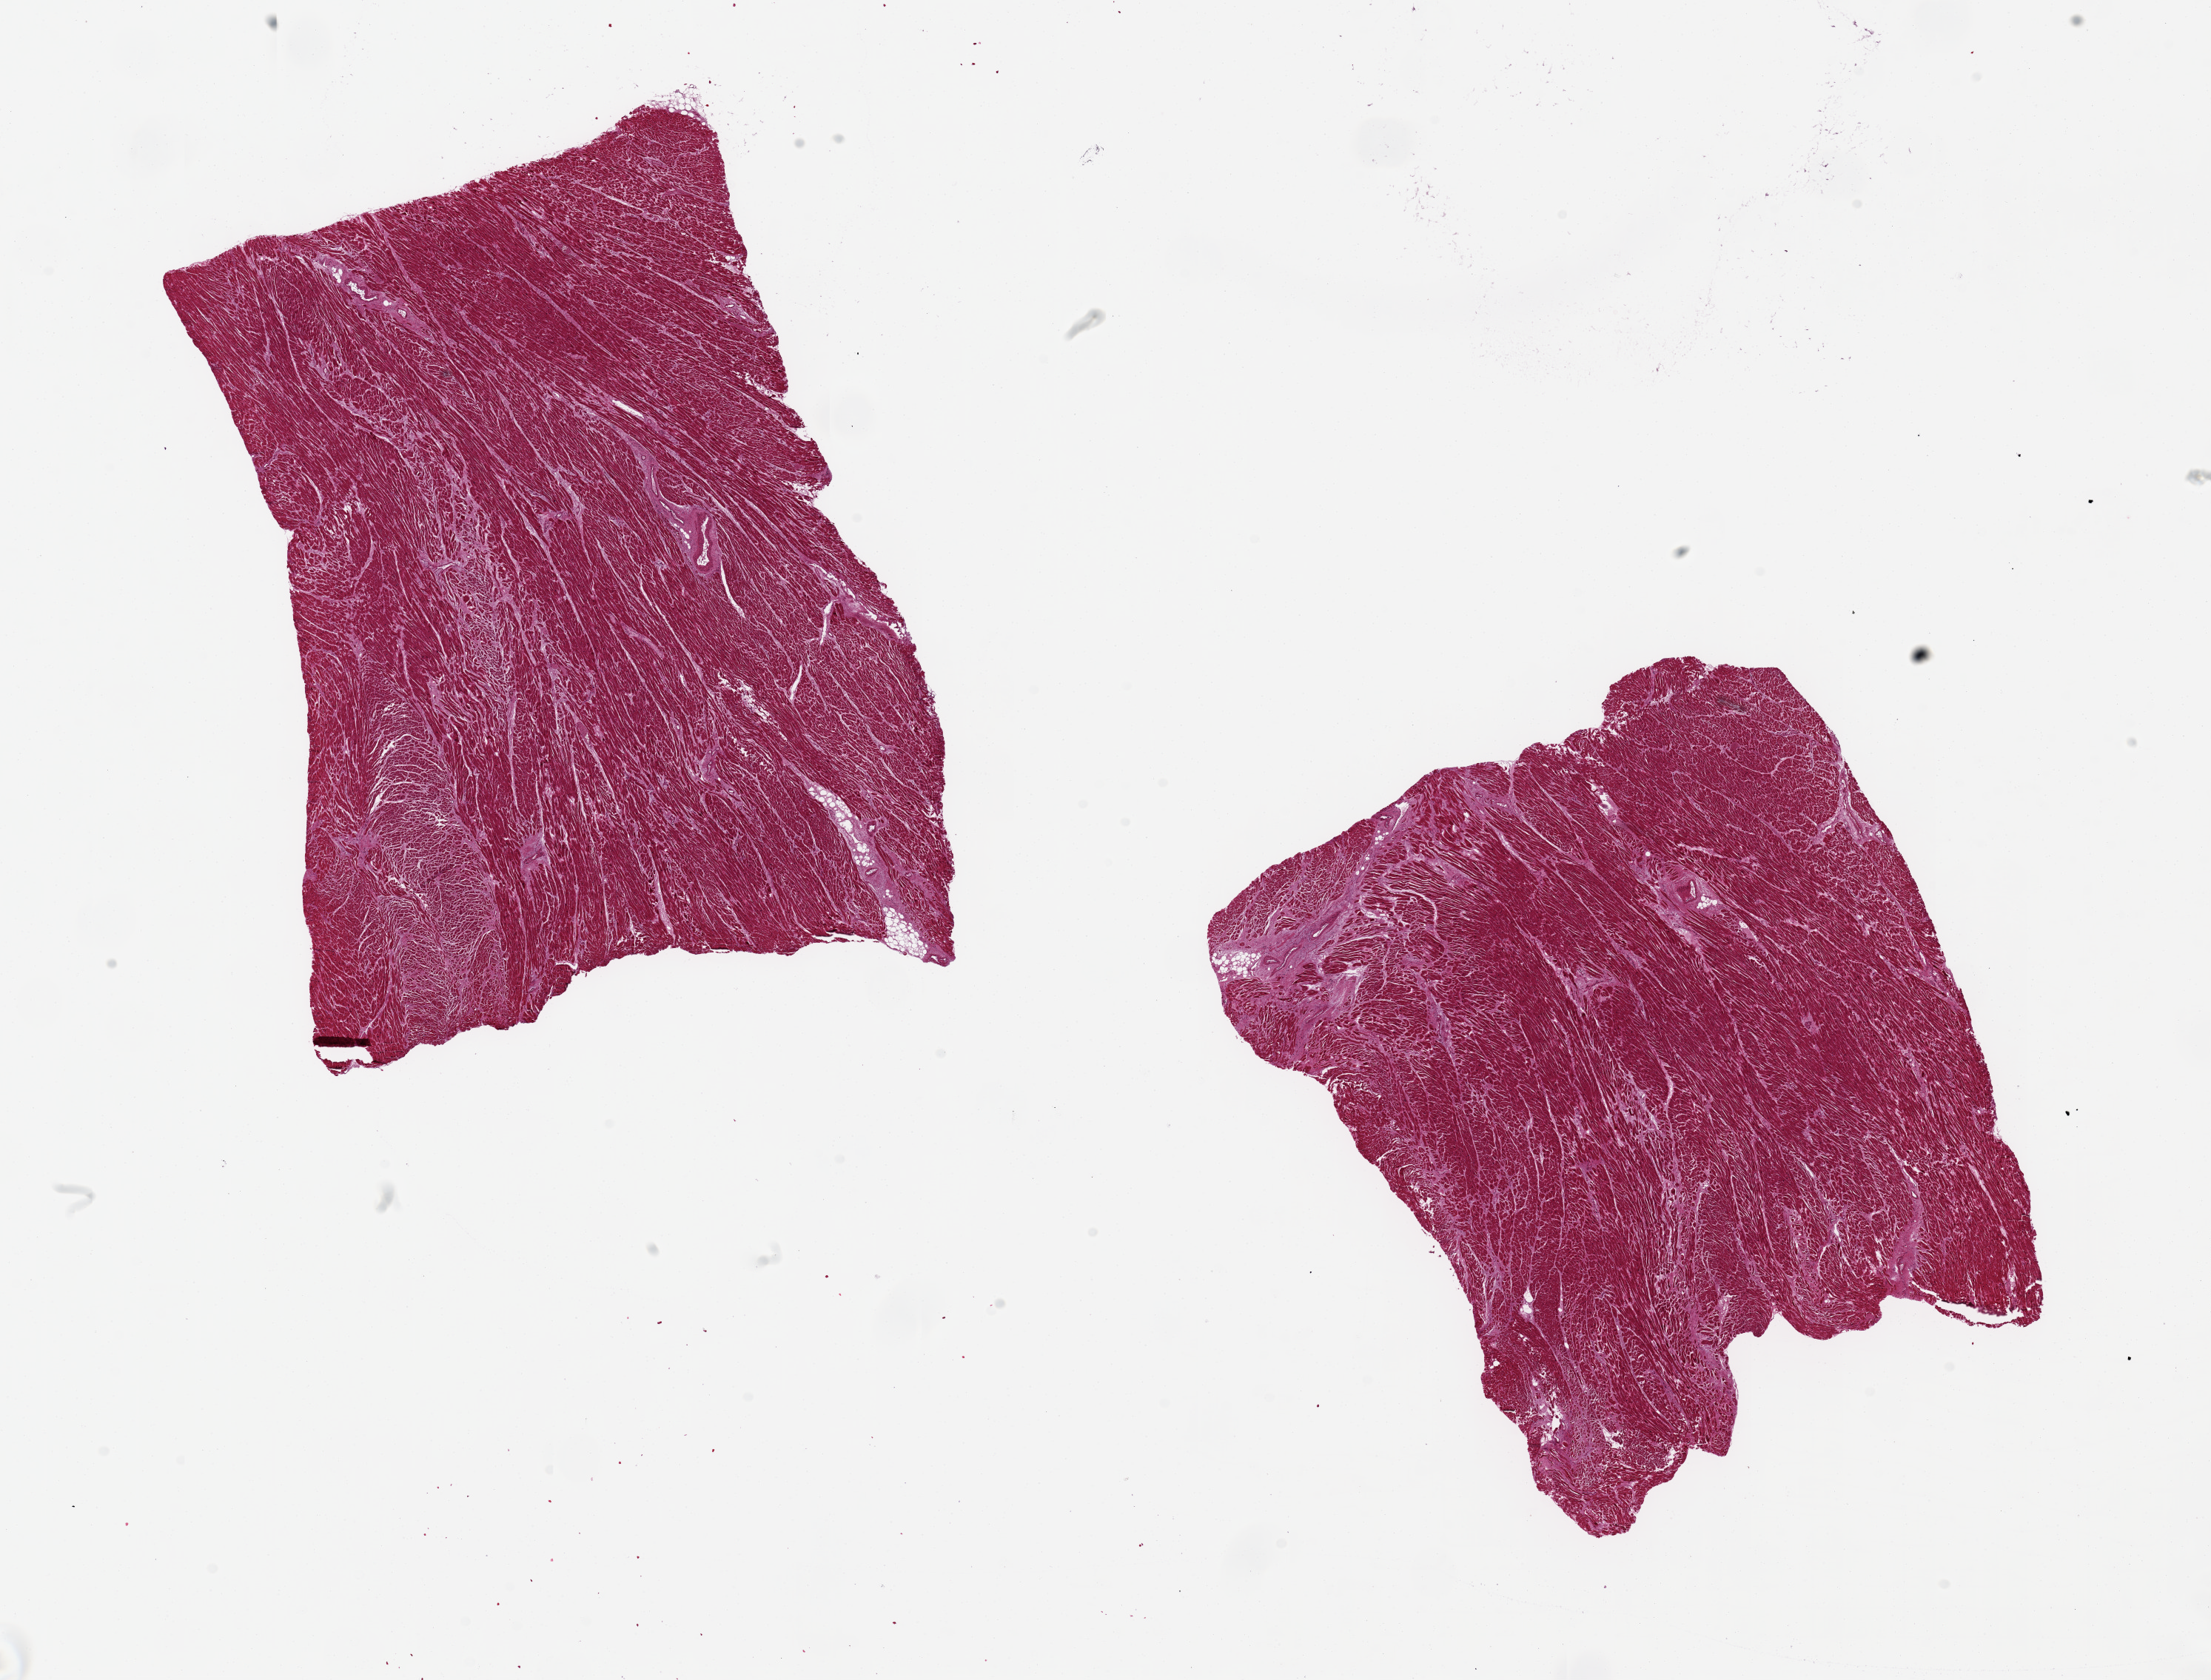
Whole-slide image, haematoxylin and eosin stain, brightfield — a low-resolution overview of the entire scanned area, about 23.6 x 18.0 mm; PAXgene-fixed, paraffin-embedded tissue; sampled site (target tissue): heart; tissue donor sample. Donor sex: male.
- review note (as recorded): 2 pieces, 10x7 & 8x7mm; mild patchy fibrosis